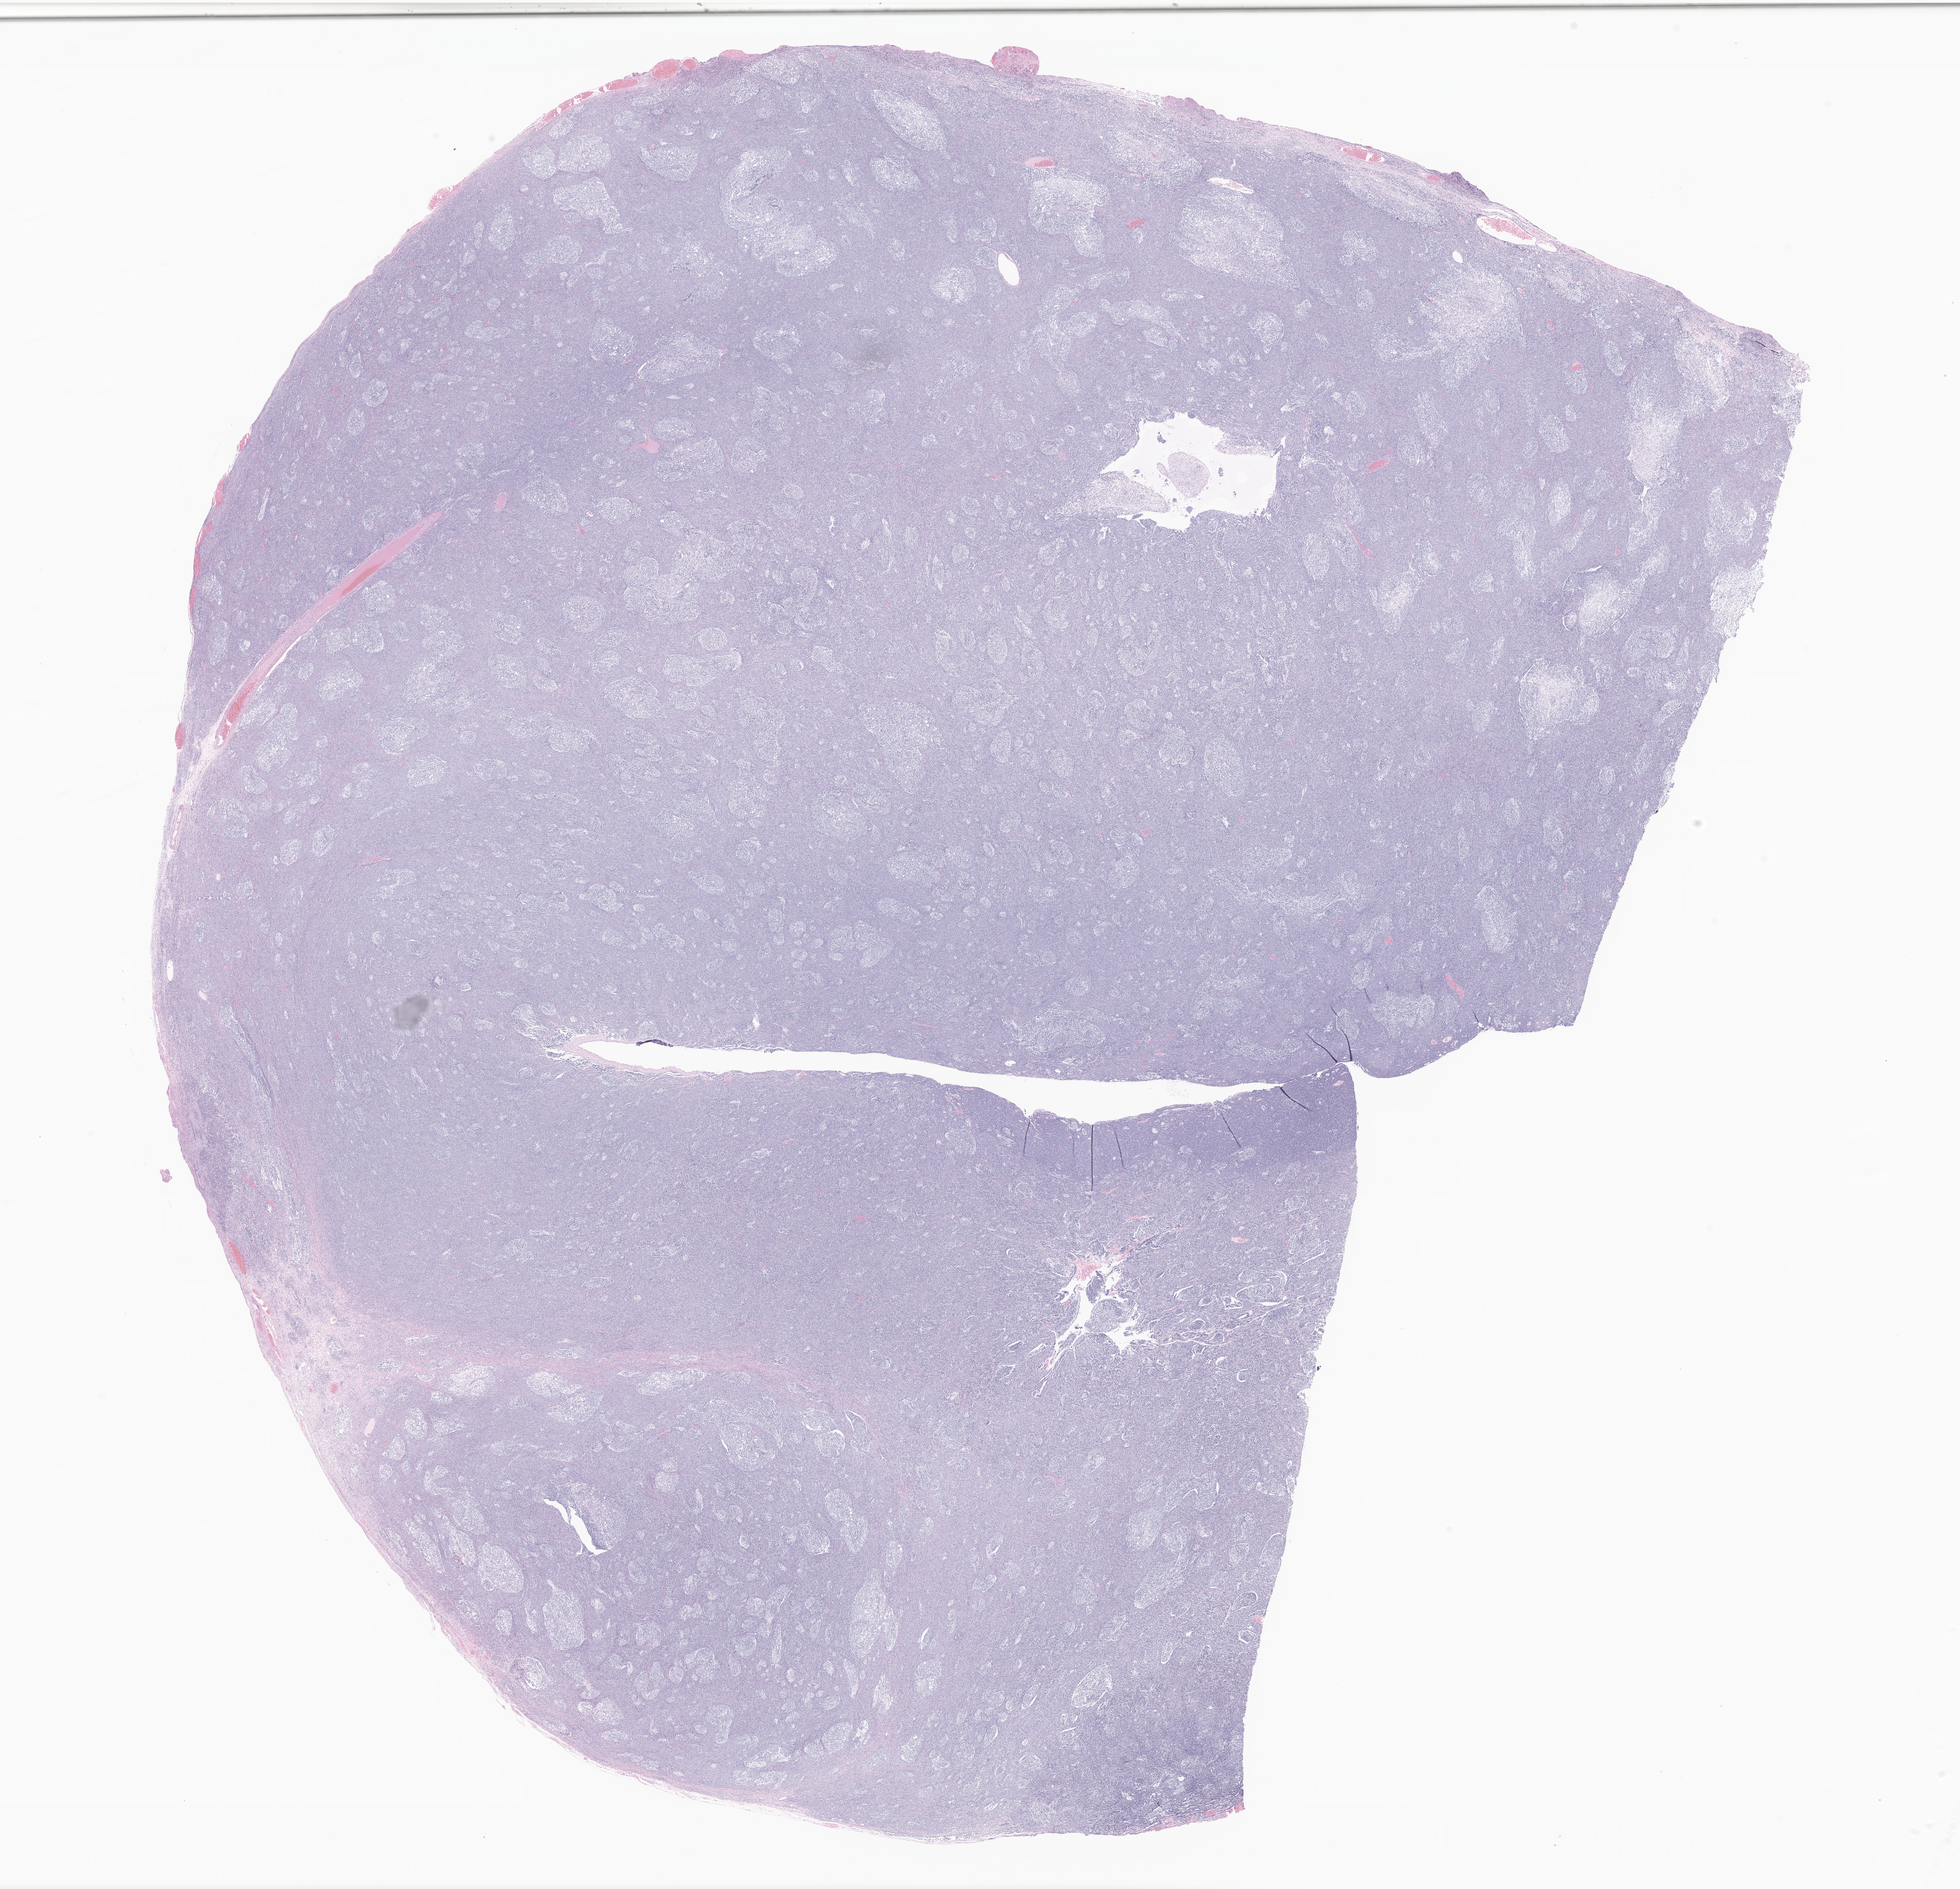
Digitized H&E-stained section of tumor tissue from the cerebellum, low-resolution overview of the scanned area, about 24.1 x 23.2 mm; formalin-fixed paraffin-embedded section. Patient female; age 638 days (about 1.7 years).
Diagnosis (ICD-O-3 morphology term): Medulloblastoma, NOS.